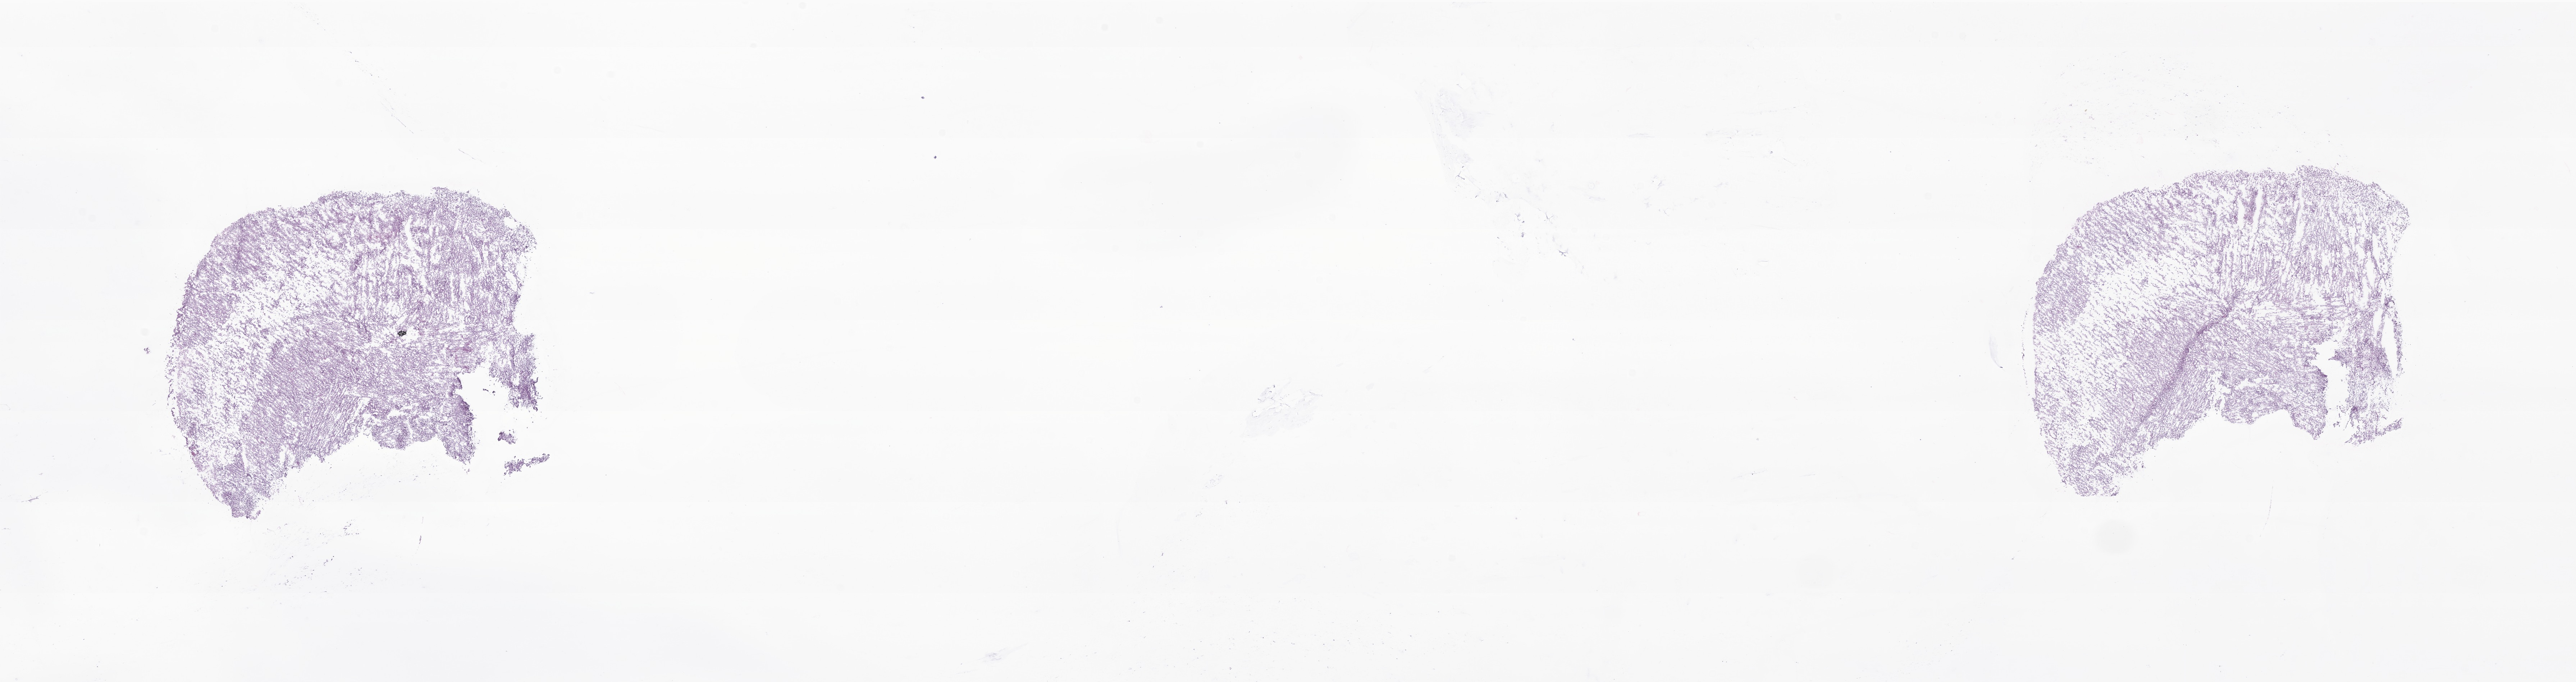
Haematoxylin and eosin whole-slide image of tumor tissue from the brain — whole scanned area (about 30.2 x 8.0 mm) shown as a low-resolution overview. Frozen section. Patient: male, age 546 days (about 1.5 years).
- diagnosis (ICD-O-3 morphology term): Glioma, malignant